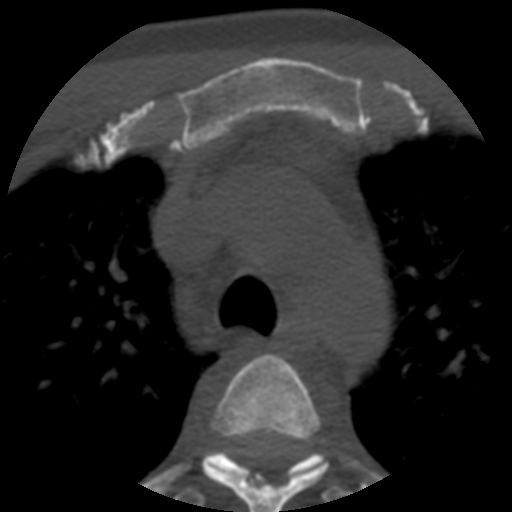
CT including the spine, one axial slice. Slice 408 of 508 in the series (ordered by position). Reconstruction kernel STANDARD. Bone window (W 1800 / L 400 HU). 1.25 mm slice thickness. 512 × 512 image matrix, field of view 160 × 160 mm. Patient age 57 years. Case-level facts recorded for this patient, not image findings: primary cancer: prostate.
Outlined on this slice (semi-automatically segmented with operator editing):
- T3 vertebra: box from (x=202, y=354) to (x=328, y=512) px
- T4 vertebra: (x=177, y=450)–(x=349, y=504)